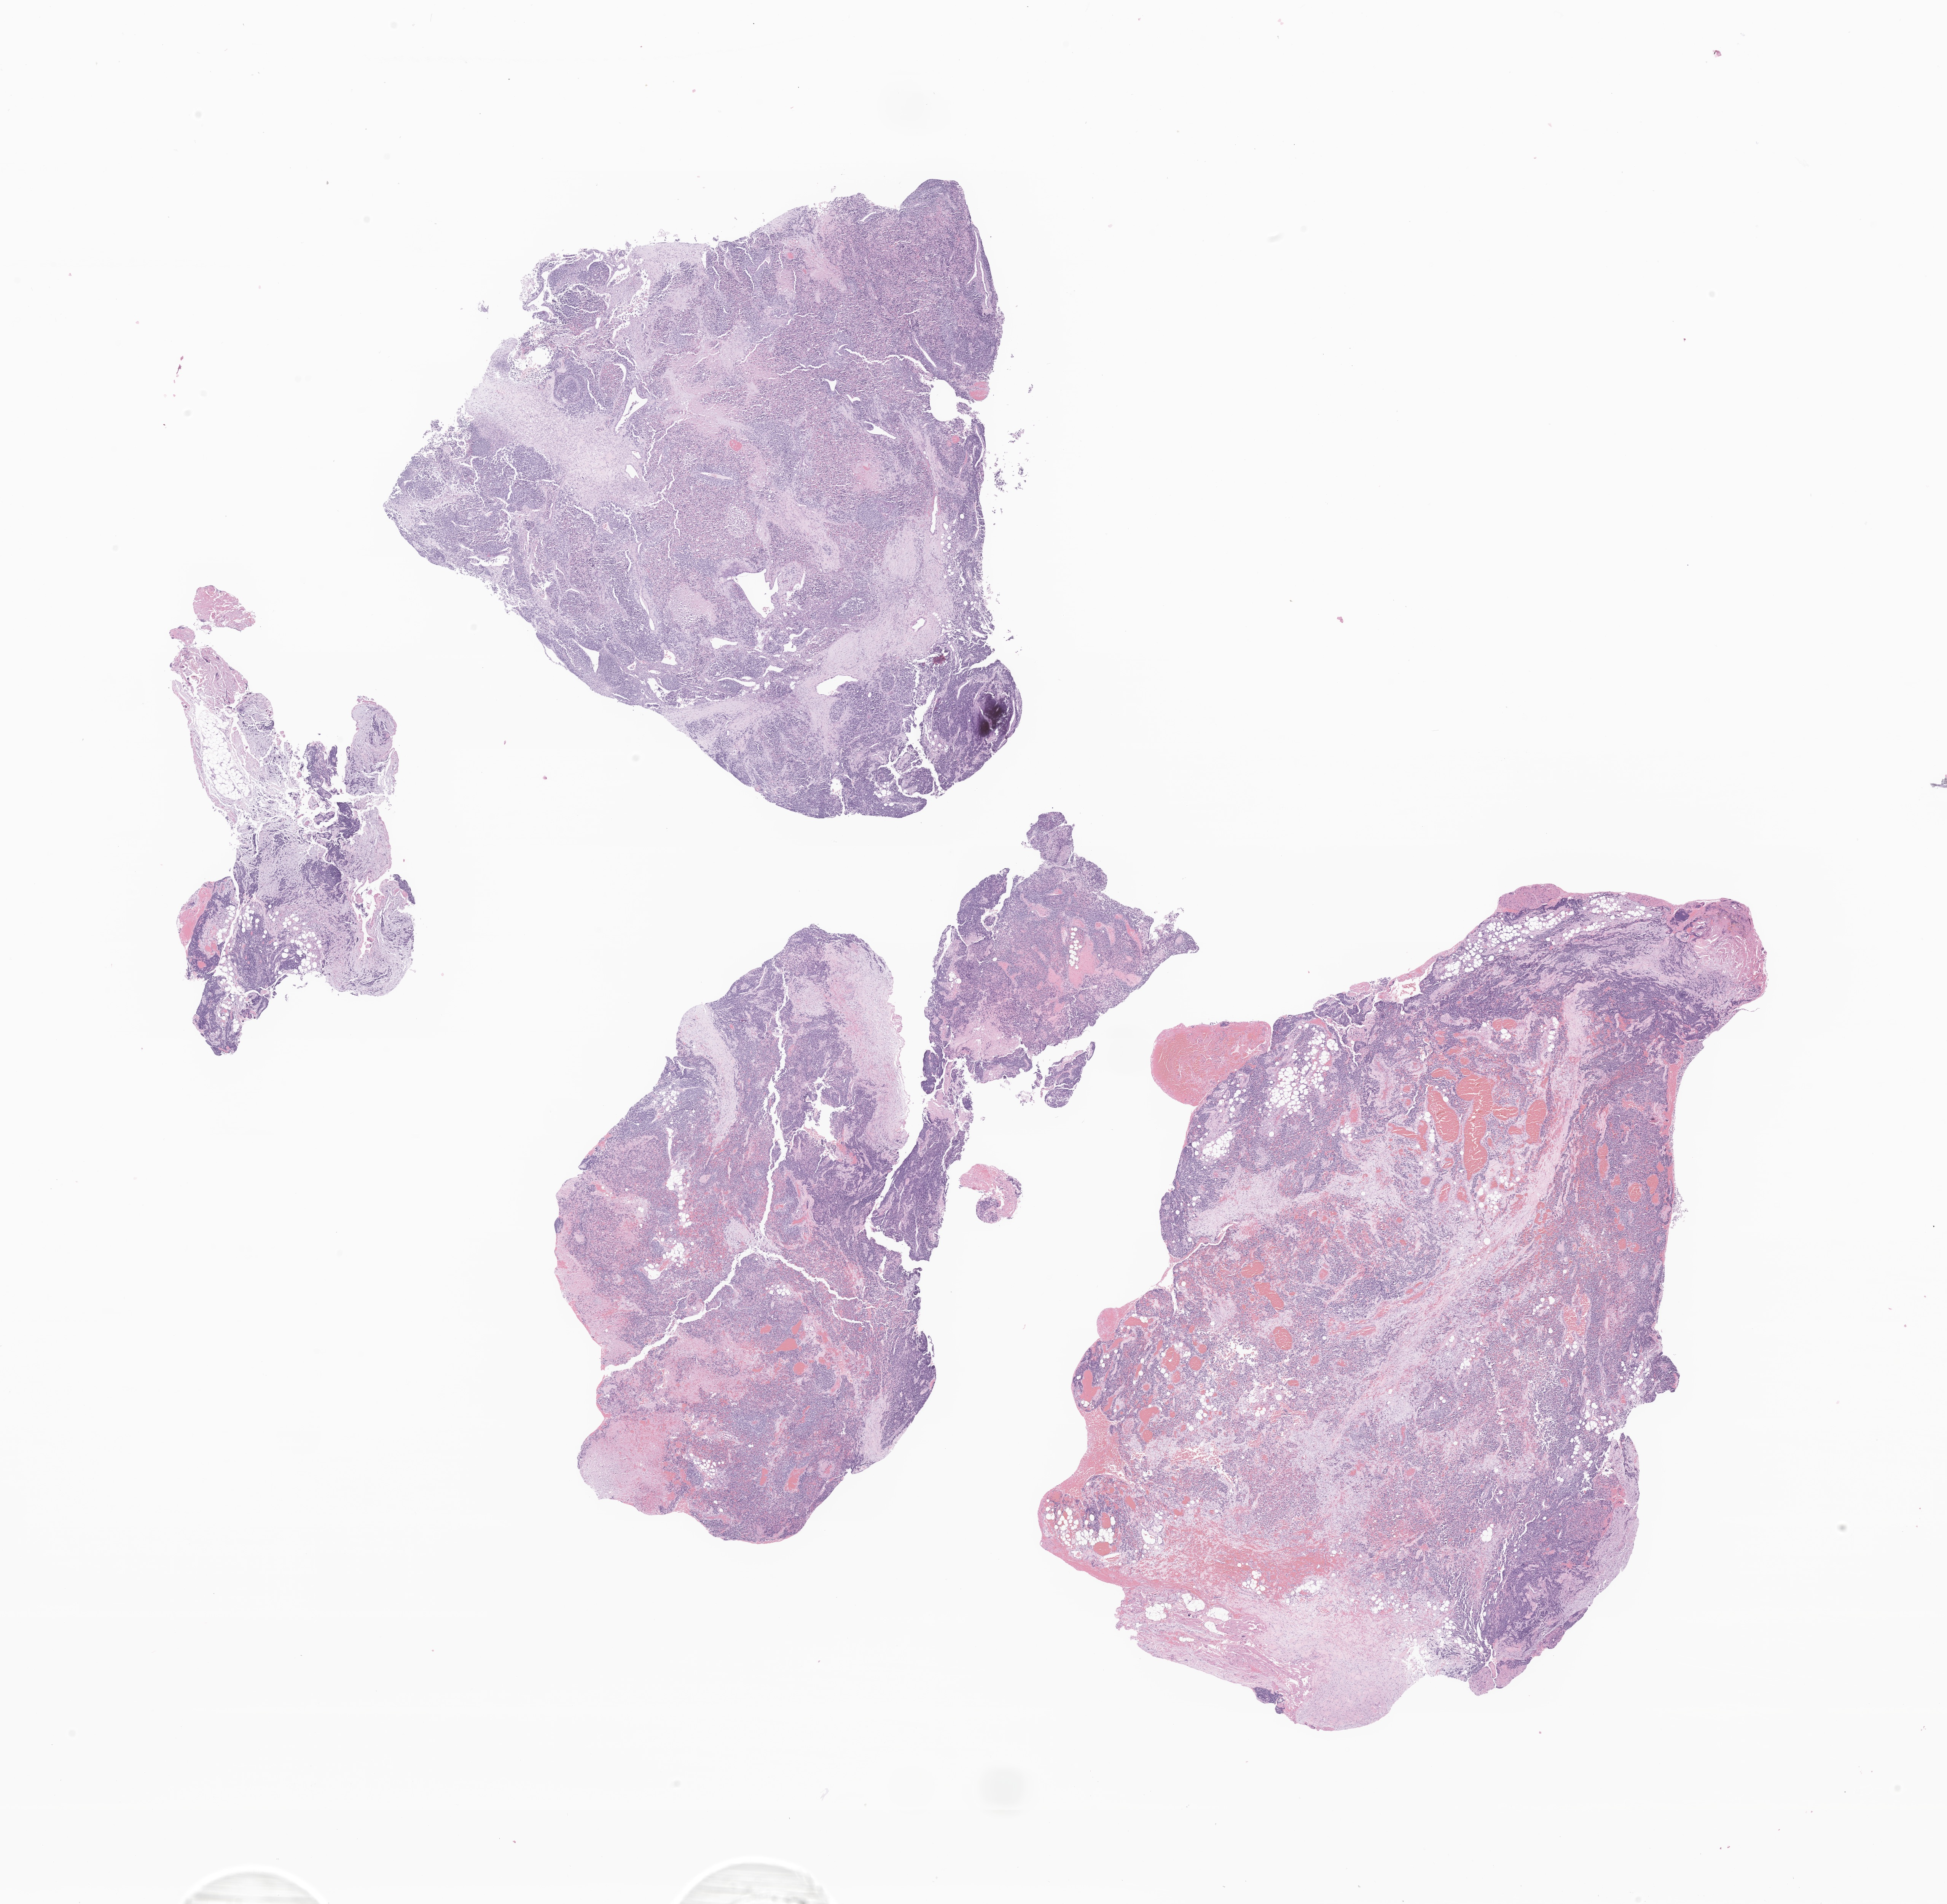
Haematoxylin and eosin whole-slide image of tumor tissue from the peritoneum, low-resolution overview of the scanned area, about 21.6 x 21.1 mm, formalin-fixed paraffin-embedded section. Male patient, age 103 months (8 years 7 months).
- diagnosis: Rhabdomyosarcoma, NOS